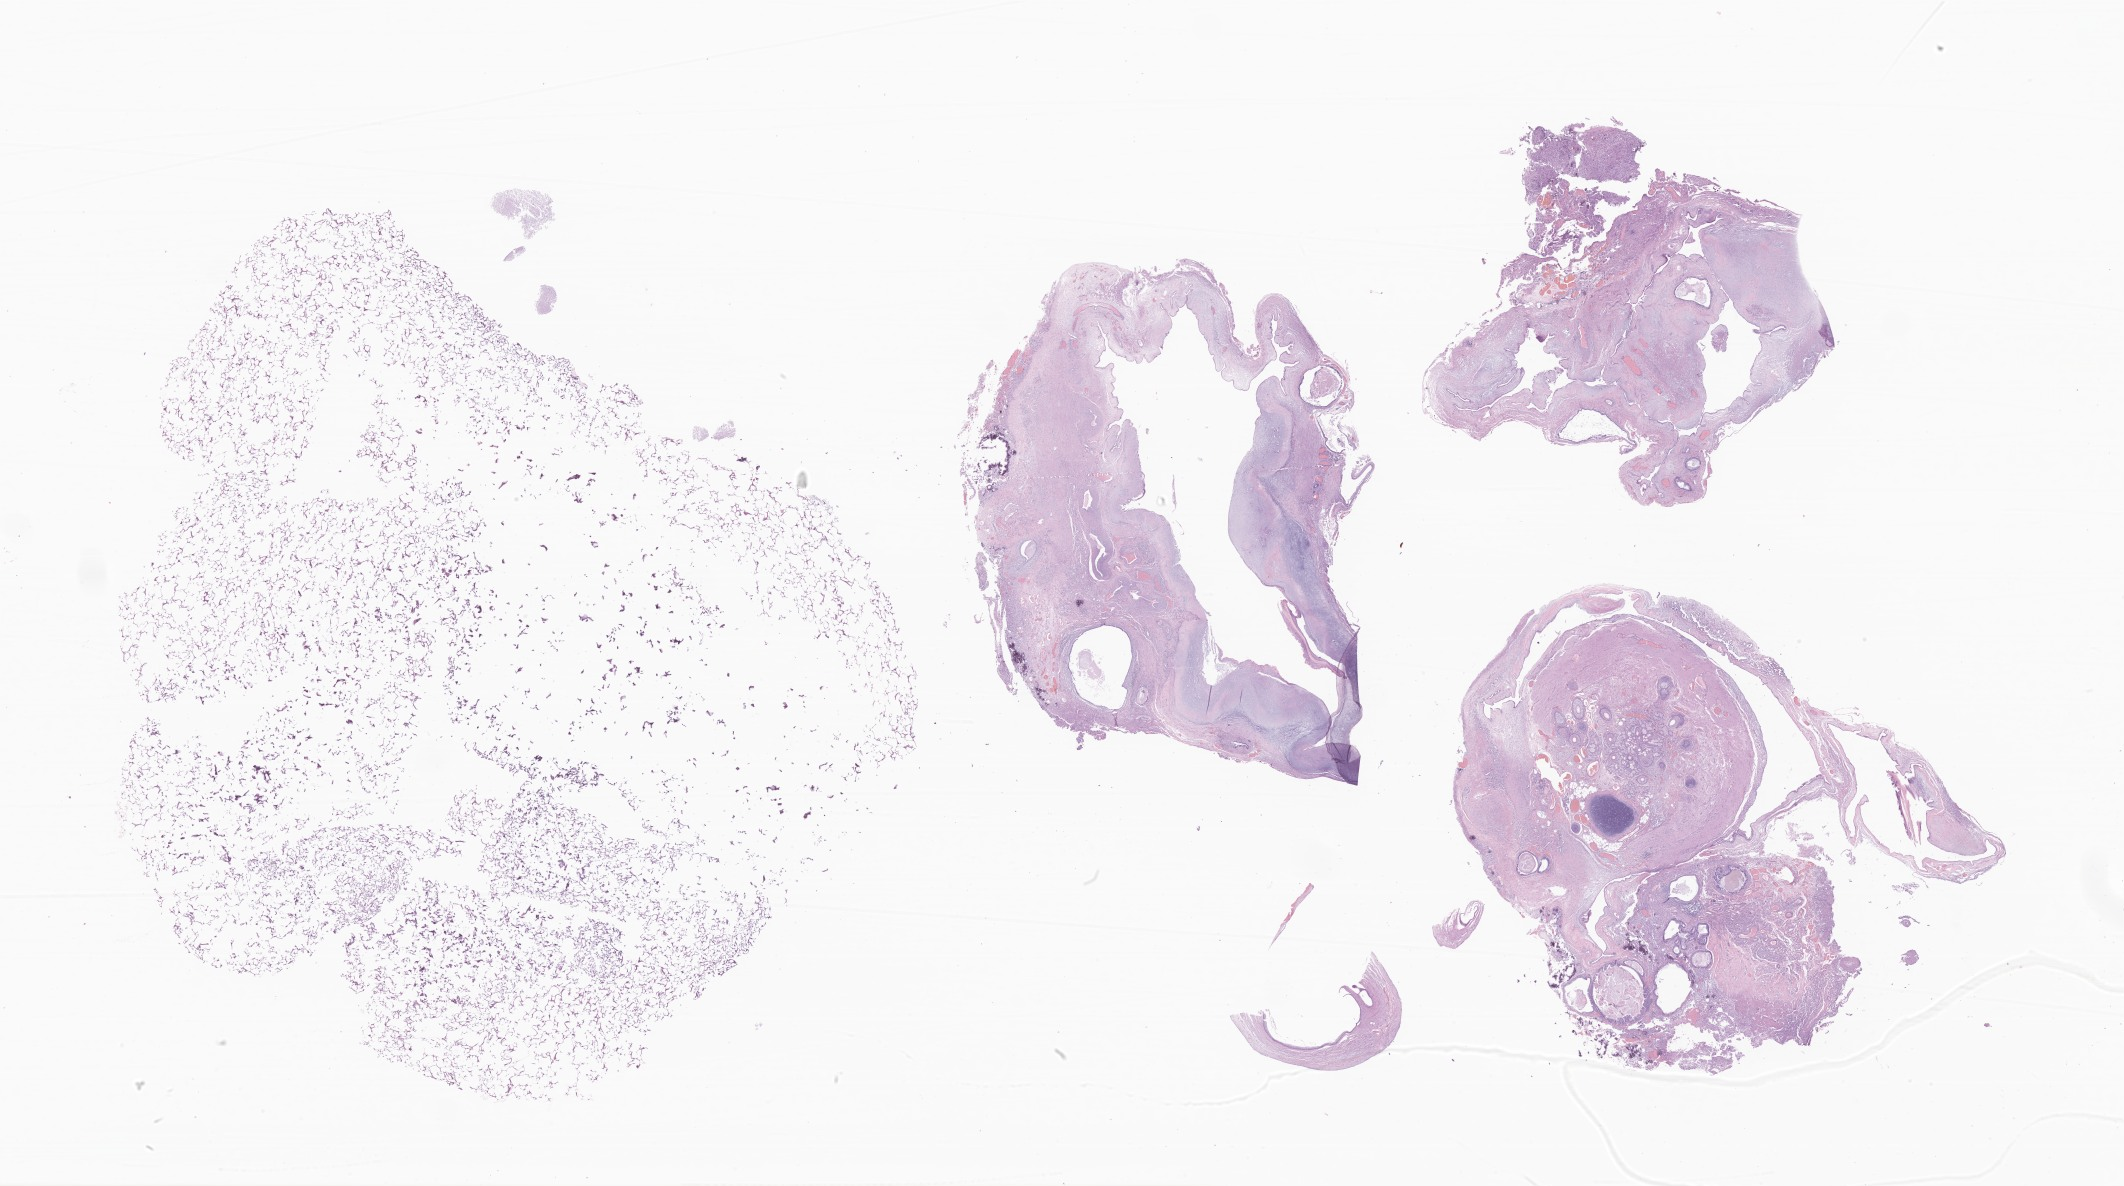
Whole-slide image, haematoxylin and eosin stain of tumor tissue from the pineal gland, shown as a low-resolution overview of the whole scanned area (about 35.8 x 20.0 mm); formalin-fixed paraffin-embedded section. Patient: male, age 69 months (5 years 9 months).
Diagnosis (ICD-O-3 morphology term): Mixed germ cell tumor.